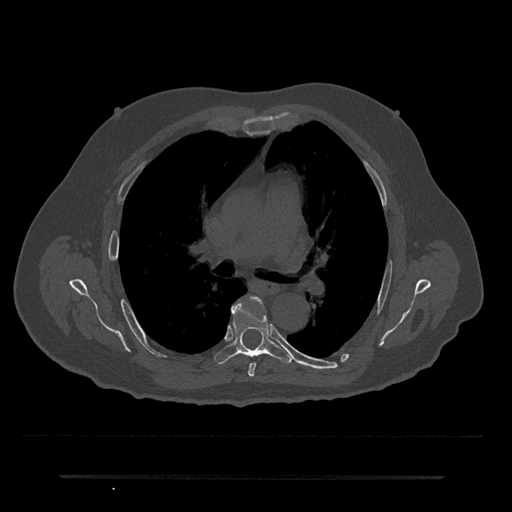
CT including the spine, one axial slice; position 449 of 797 along the scan axis; 120 kVp; bone window (W 1800 / L 400 HU); 0.5 mm slice thickness; 512 × 512 image matrix, field of view 437 × 437 mm. Patient: male, 69 years. From the clinical record (not read from this slice): primary cancer: prostate.
Outlined on this slice (semi-automatic segmentation, software-assisted and operator-edited):
- T5 vertebra: bounding box (x1, y1, x2, y2) in pixels: (248, 297, 263, 377)
- T6 vertebra: (214, 301, 293, 364)